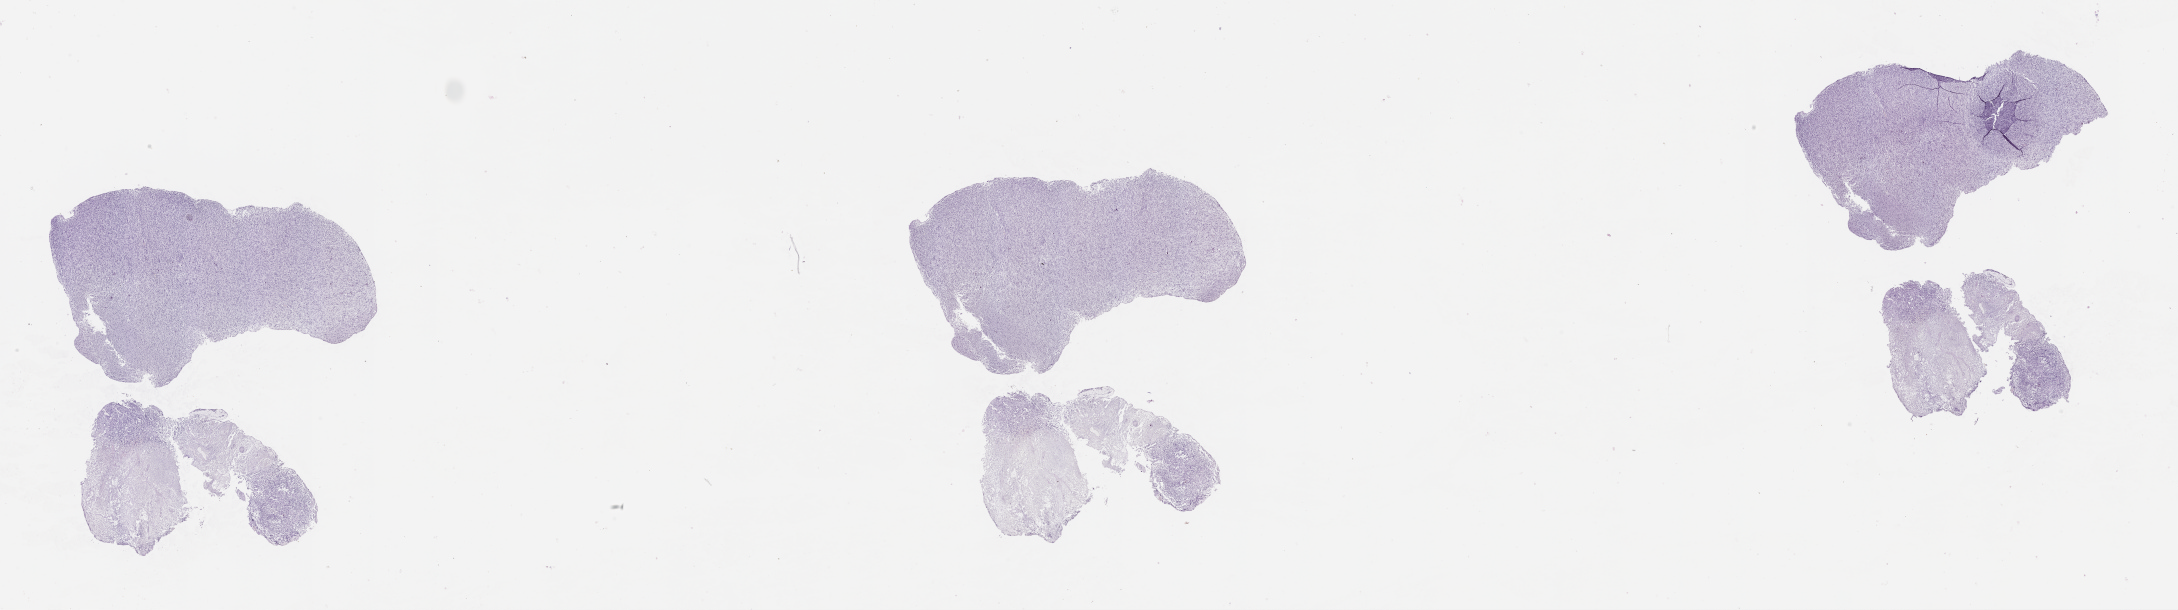
Whole-slide histology image, Hematoxylin and eosin (H&E) stained, whole scanned area (about 35.1 x 9.8 mm) shown as a low-resolution overview, tumour tissue sample, brain. 81-year-old female patient.
Primary tumour site (as recorded): parietal lobe. Histologic diagnosis: Glioblastoma.